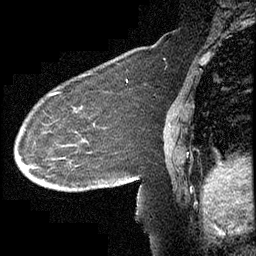
Breast MRI (dynamic contrast-enhanced), one sagittal slice. Slice 150 of 232 in the series (ordered by position). Dynamic contrast-enhanced study with each time point stored as its own series, time point 2 of 4 at this slice position (early post-contrast, ordered by acquisition time). 1.5 T. TE 4.2 ms, TR 6.7 ms. 256 × 256 image matrix, field of view 200 × 200 mm. Female patient, age 63 years. From the clinical record (not read from this slice): setting: breast cancer imaged before/during neoadjuvant chemotherapy; receptor status: triple-negative.
Outlined on this slice (semi-automatically segmented with operator editing):
- analysis volume of interest (the breast-tissue region the enhancement analysis was run in; not a lesion): bounding box (x1, y1, x2, y2) in pixels: (14, 90, 140, 211)
- tumour enhancement mask (voxels above the 70 % enhancement threshold inside the analysis volume of interest): (55, 92, 58, 94)